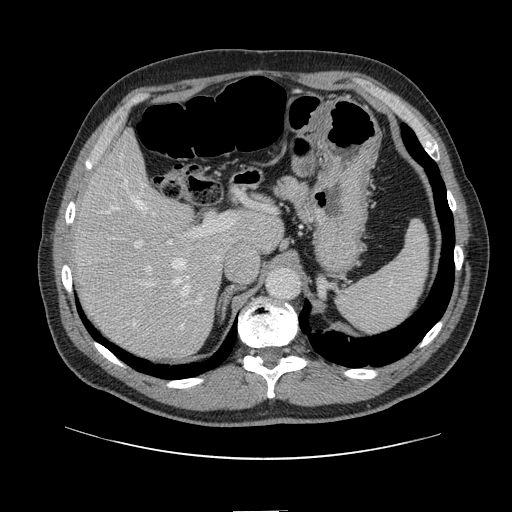
Contrast-enhanced abdominal CT, one axial slice; position 92 of 161 along the scan axis; soft-tissue window (W 400 / L 40 HU); 2.5 mm slice thickness; 512 × 512 image matrix, field of view 412 × 412 mm. Male patient, age 66 years. From the clinical record (not read from this slice): diagnosis: colorectal cancer liver metastases, imaged before liver resection; multiple liver metastases: no; largest metastasis: 3.5 cm.
Structures marked on this image (expert manual segmentation):
- hepatic veins: box from (x=103, y=157) to (x=189, y=325) px
- liver: (x=76, y=136)–(x=280, y=358)
- planned liver remnant (the part of the liver to remain after resection): (x=76, y=136)–(x=281, y=305)
- portal vein (with intrahepatic branches): (x=134, y=216)–(x=234, y=307)